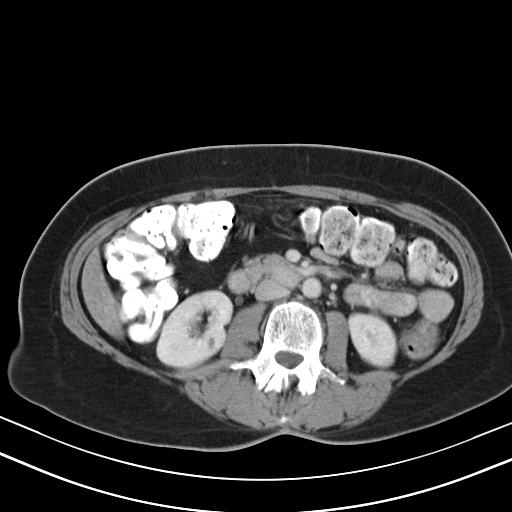
Contrast-enhanced abdominal CT, one axial slice. Slice 15 of 47 in the series (ordered by position). Reconstruction kernel B40s. Soft-tissue window (W 400 / L 40 HU). 5 mm slice thickness. 512 × 512 image matrix. Female patient. Case-level facts recorded for this patient, not image findings: diagnosis: colorectal cancer liver metastases, imaged before liver resection; multiple liver metastases: no; largest metastasis: 3.5 cm; disease in both lobes: no.
Annotated regions visible in this slice (outlined manually by an expert reader):
- liver: bounding box (x1, y1, x2, y2) in pixels: (85, 259, 118, 331)
- planned liver remnant (the part of the liver to remain after resection): (84, 258, 118, 331)